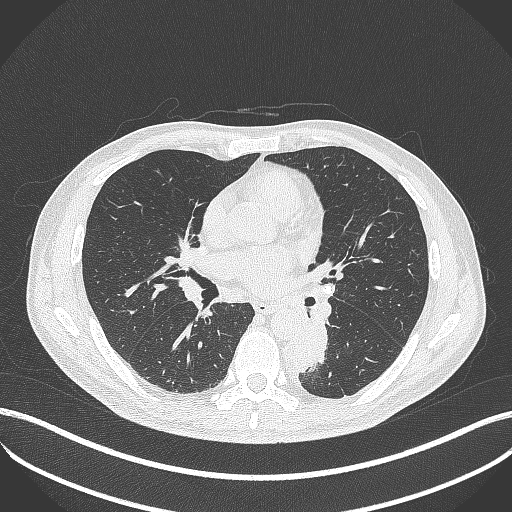
Chest CT, one axial slice; slice 212 of 451 in the series (ordered by position); lung window (W 1500 / L -600 HU); 512 × 512 image matrix. Male patient, age 72 years. From the clinical record (not read from this slice): clinical TNM (as recorded): T2b N0 M1.
Outlined on this slice (bounding box drawn by a radiologist):
- lung tumour (recorded histology: adenocarcinoma): bounding box <286,321,335,375> (left, top, right, bottom; pixels)